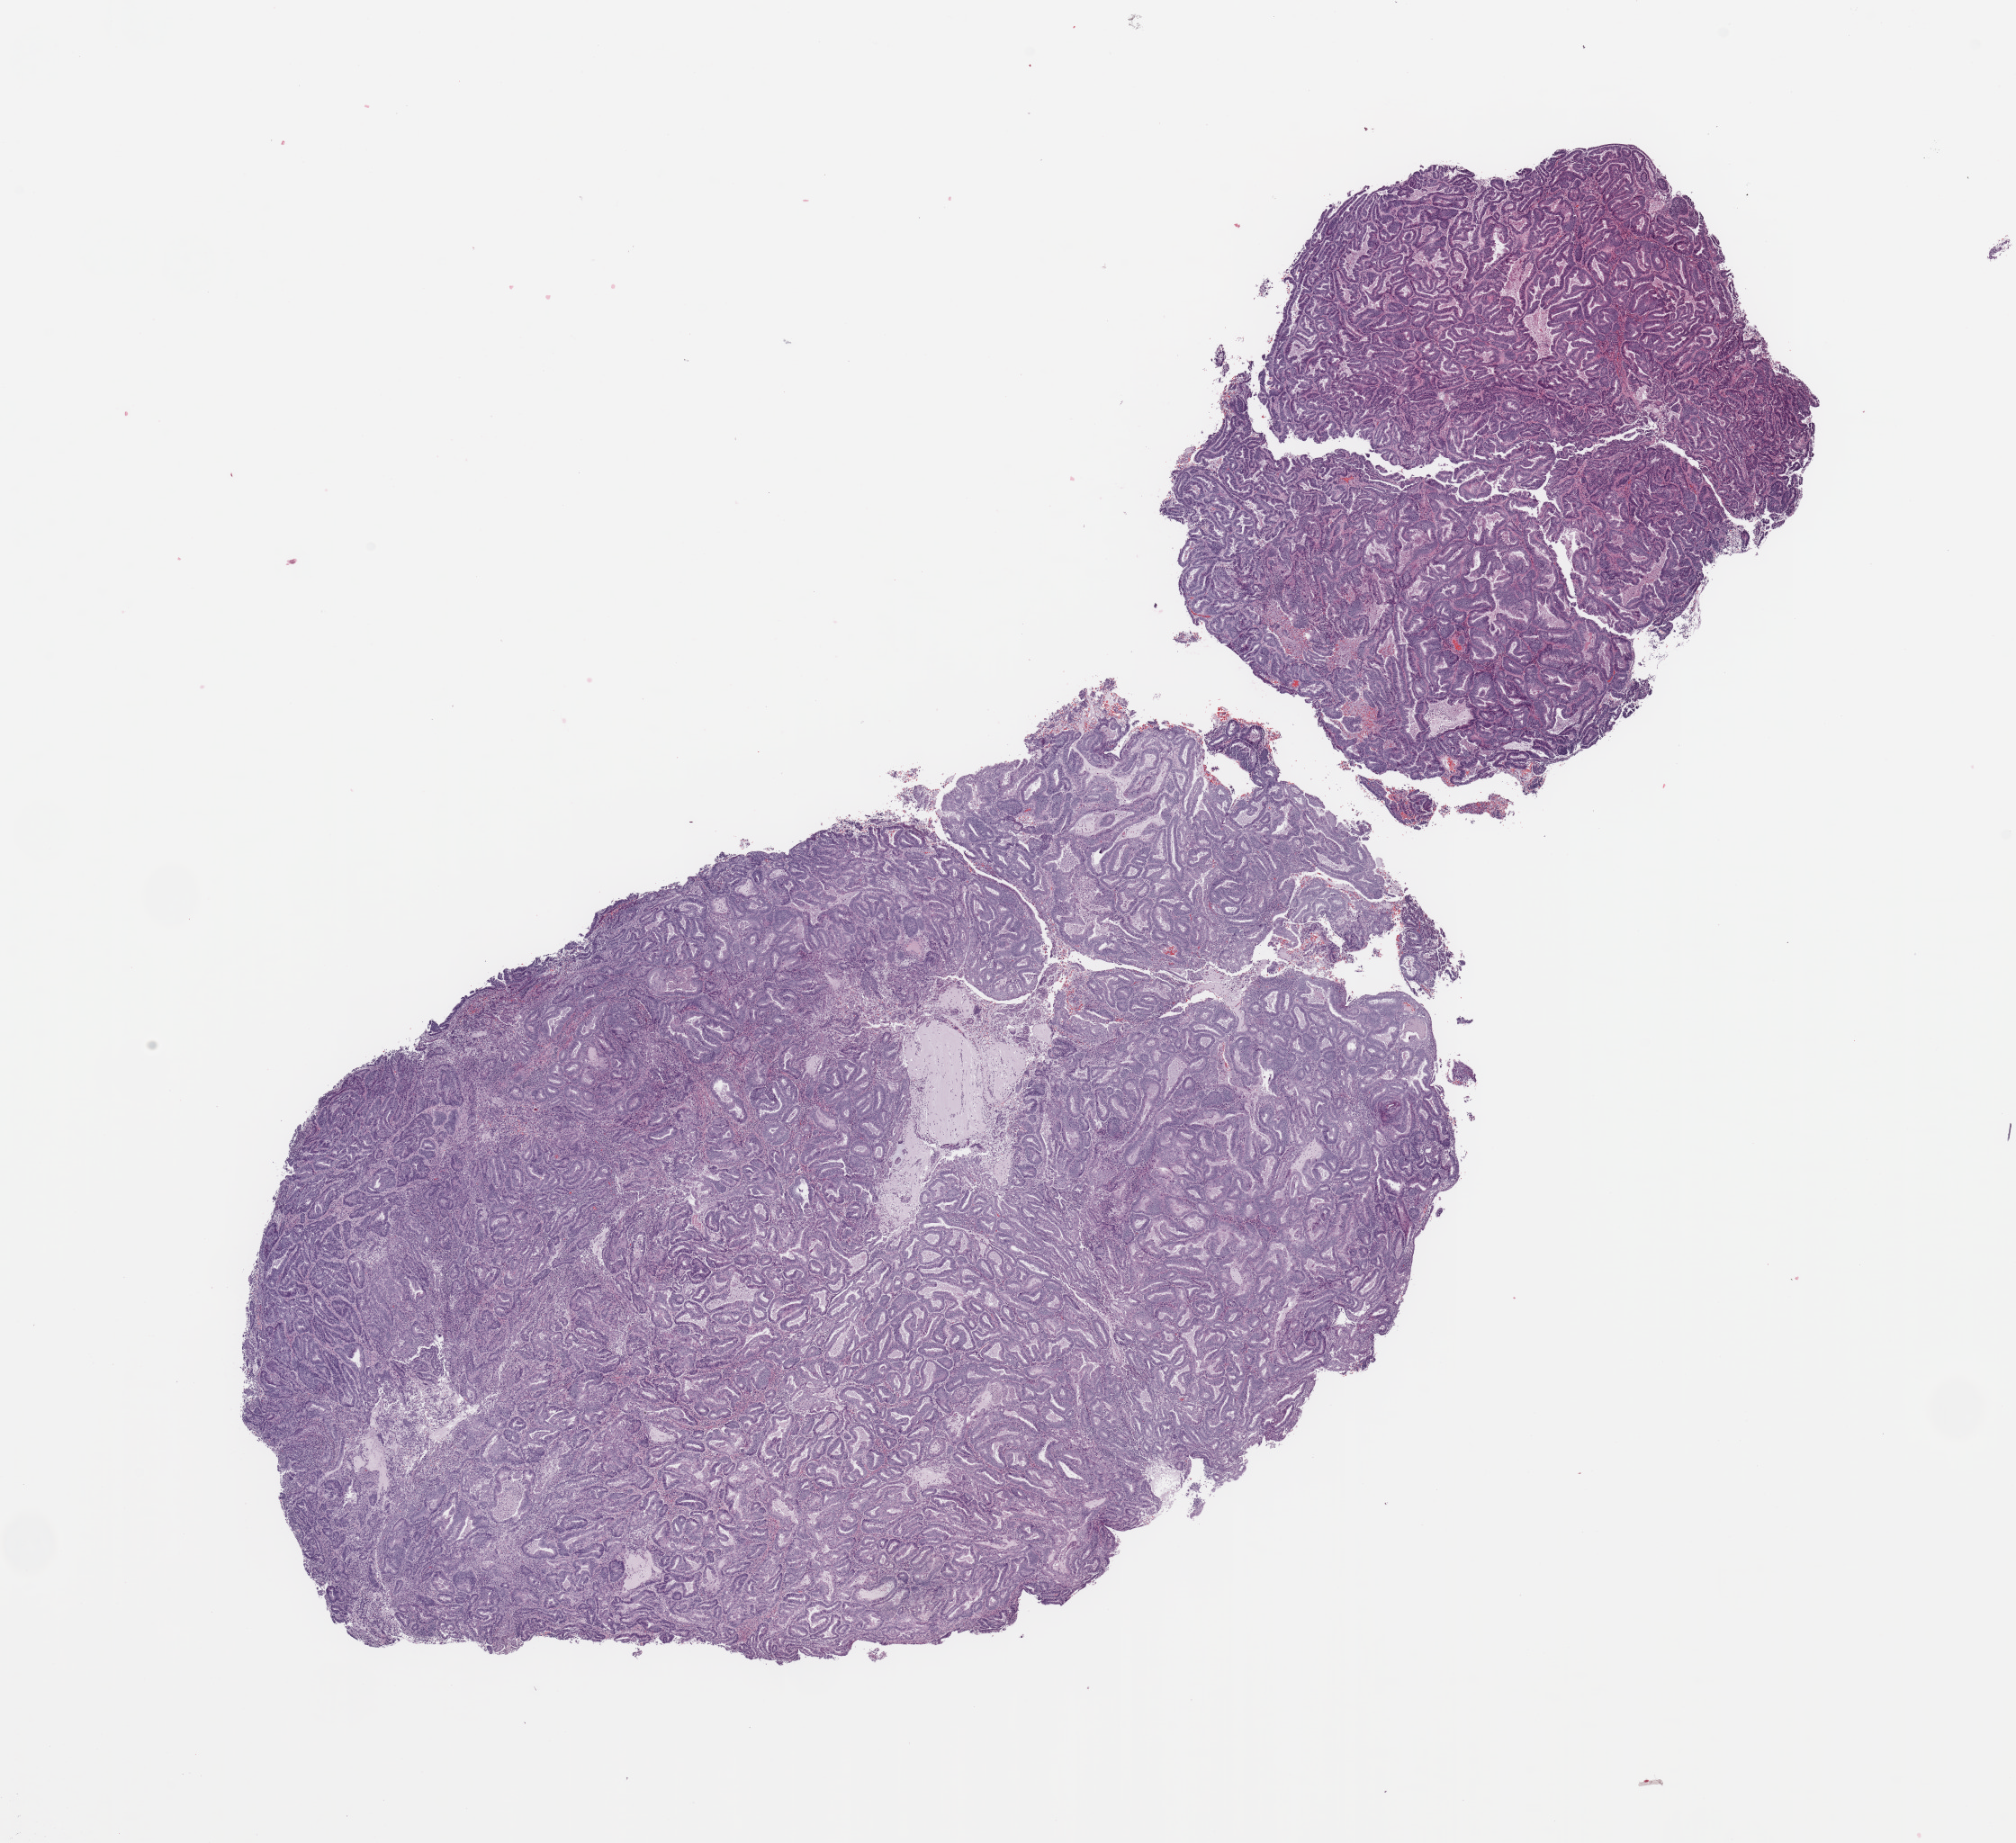
Whole-slide histology image, H&E — whole scanned area (about 17.7 x 16.2 mm, from a 20x scan) shown as a low-resolution overview, tumour tissue sample, sampled site: uterus. Patient: female, age 62 years. Histologic grade: G1 (well differentiated). Pathologist review of this section (percent, as recorded): tumour nuclei 90%, necrosis 2%.
Histologic diagnosis: Endometrioid adenocarcinoma, NOS. AJCC pathologic stage: I.